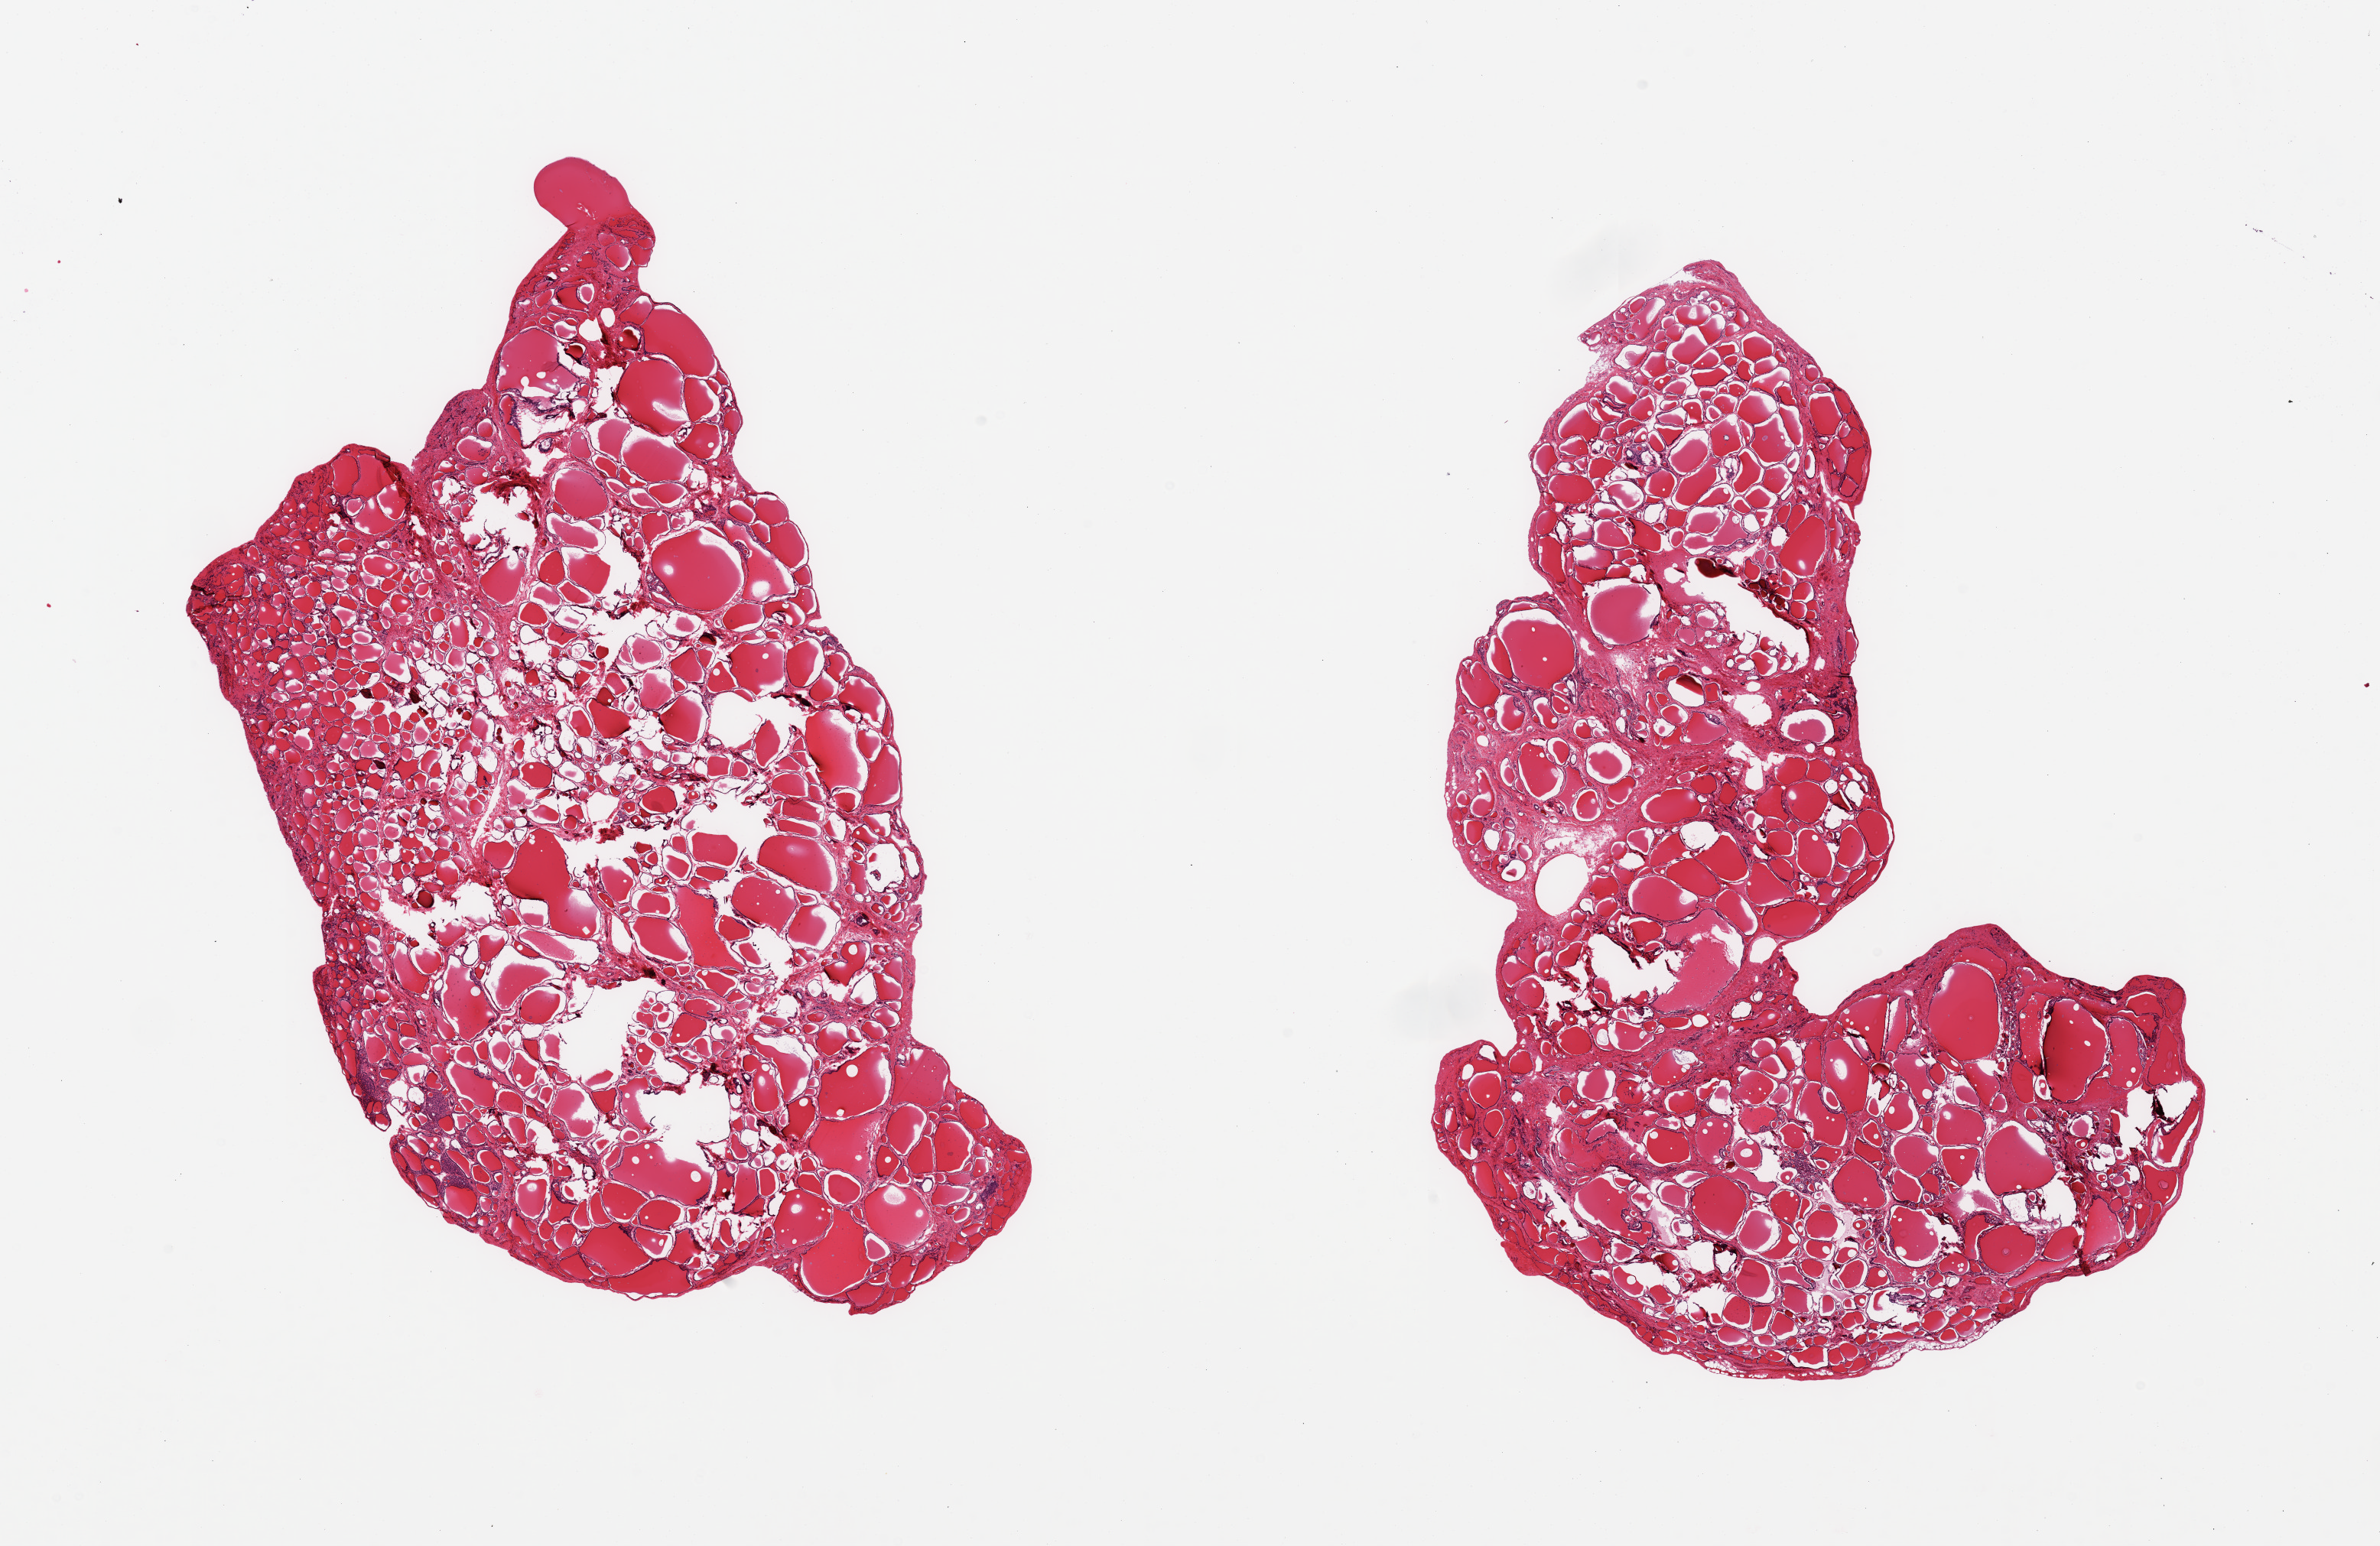
Digitized haematoxylin and eosin-stained section — a low-resolution overview of the entire scanned area, about 24.6 x 16.0 mm (from a 20x scan). PAXgene-fixed paraffin-embedded (PFPE) section. Section of thyroid (target tissue). Tissue donor sample.
Pathologist's review note for this sample: 2 pieces, no abnormalities.